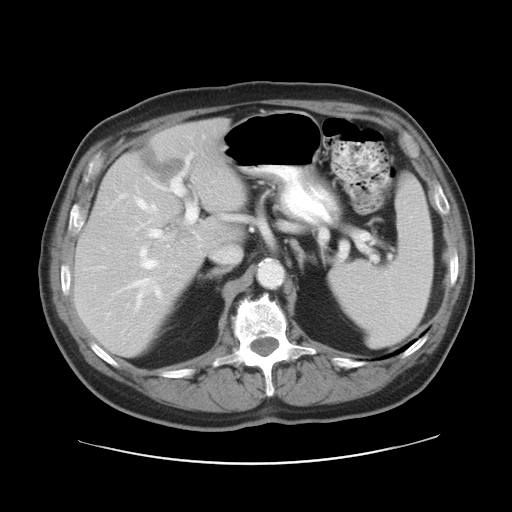
Contrast-enhanced abdominal CT, one axial slice. Slice 18 of 28 in the series (ordered by position). 120 kVp. Intravenous contrast given. Soft-tissue window (W 400 / L 40 HU). 7.5 mm slice thickness. 512 × 512 image matrix. Male patient, age 74 years. Case-level facts recorded for this patient, not image findings: diagnosis: colorectal cancer liver metastases, imaged before liver resection; multiple liver metastases: no; largest metastasis: 5 cm.
Structures marked on this image (outlined manually by an expert reader):
- hepatic veins: bounding box (x1, y1, x2, y2) in pixels: (119, 194, 194, 311)
- liver: (75, 120, 245, 356)
- planned liver remnant (the part of the liver to remain after resection): (75, 174, 205, 356)
- portal vein (with intrahepatic branches): (140, 154, 199, 263)
- liver metastasis: (147, 155, 182, 178)